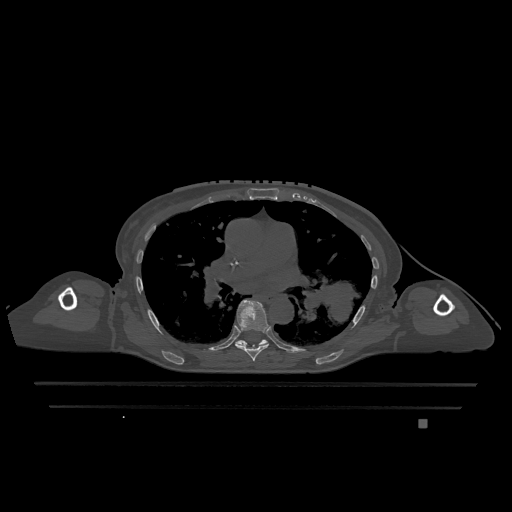
CT including the spine, one axial slice; position 772 of 1317 along the scan axis; bone window (W 1800 / L 400 HU); 512 × 512 image matrix, field of view 500 × 500 mm. Patient: female, 74 years. Case-level facts recorded for this patient, not image findings: primary cancer: lung; vertebrae with lytic lesions (as recorded): T1, T4, T5, T6, L4, L5.
Structures marked on this image (semi-automatic segmentation, software-assisted and operator-edited):
- T6 vertebra: bounding box <235,300,270,361> (left, top, right, bottom; pixels)
- T7 vertebra: <235,339,268,346>